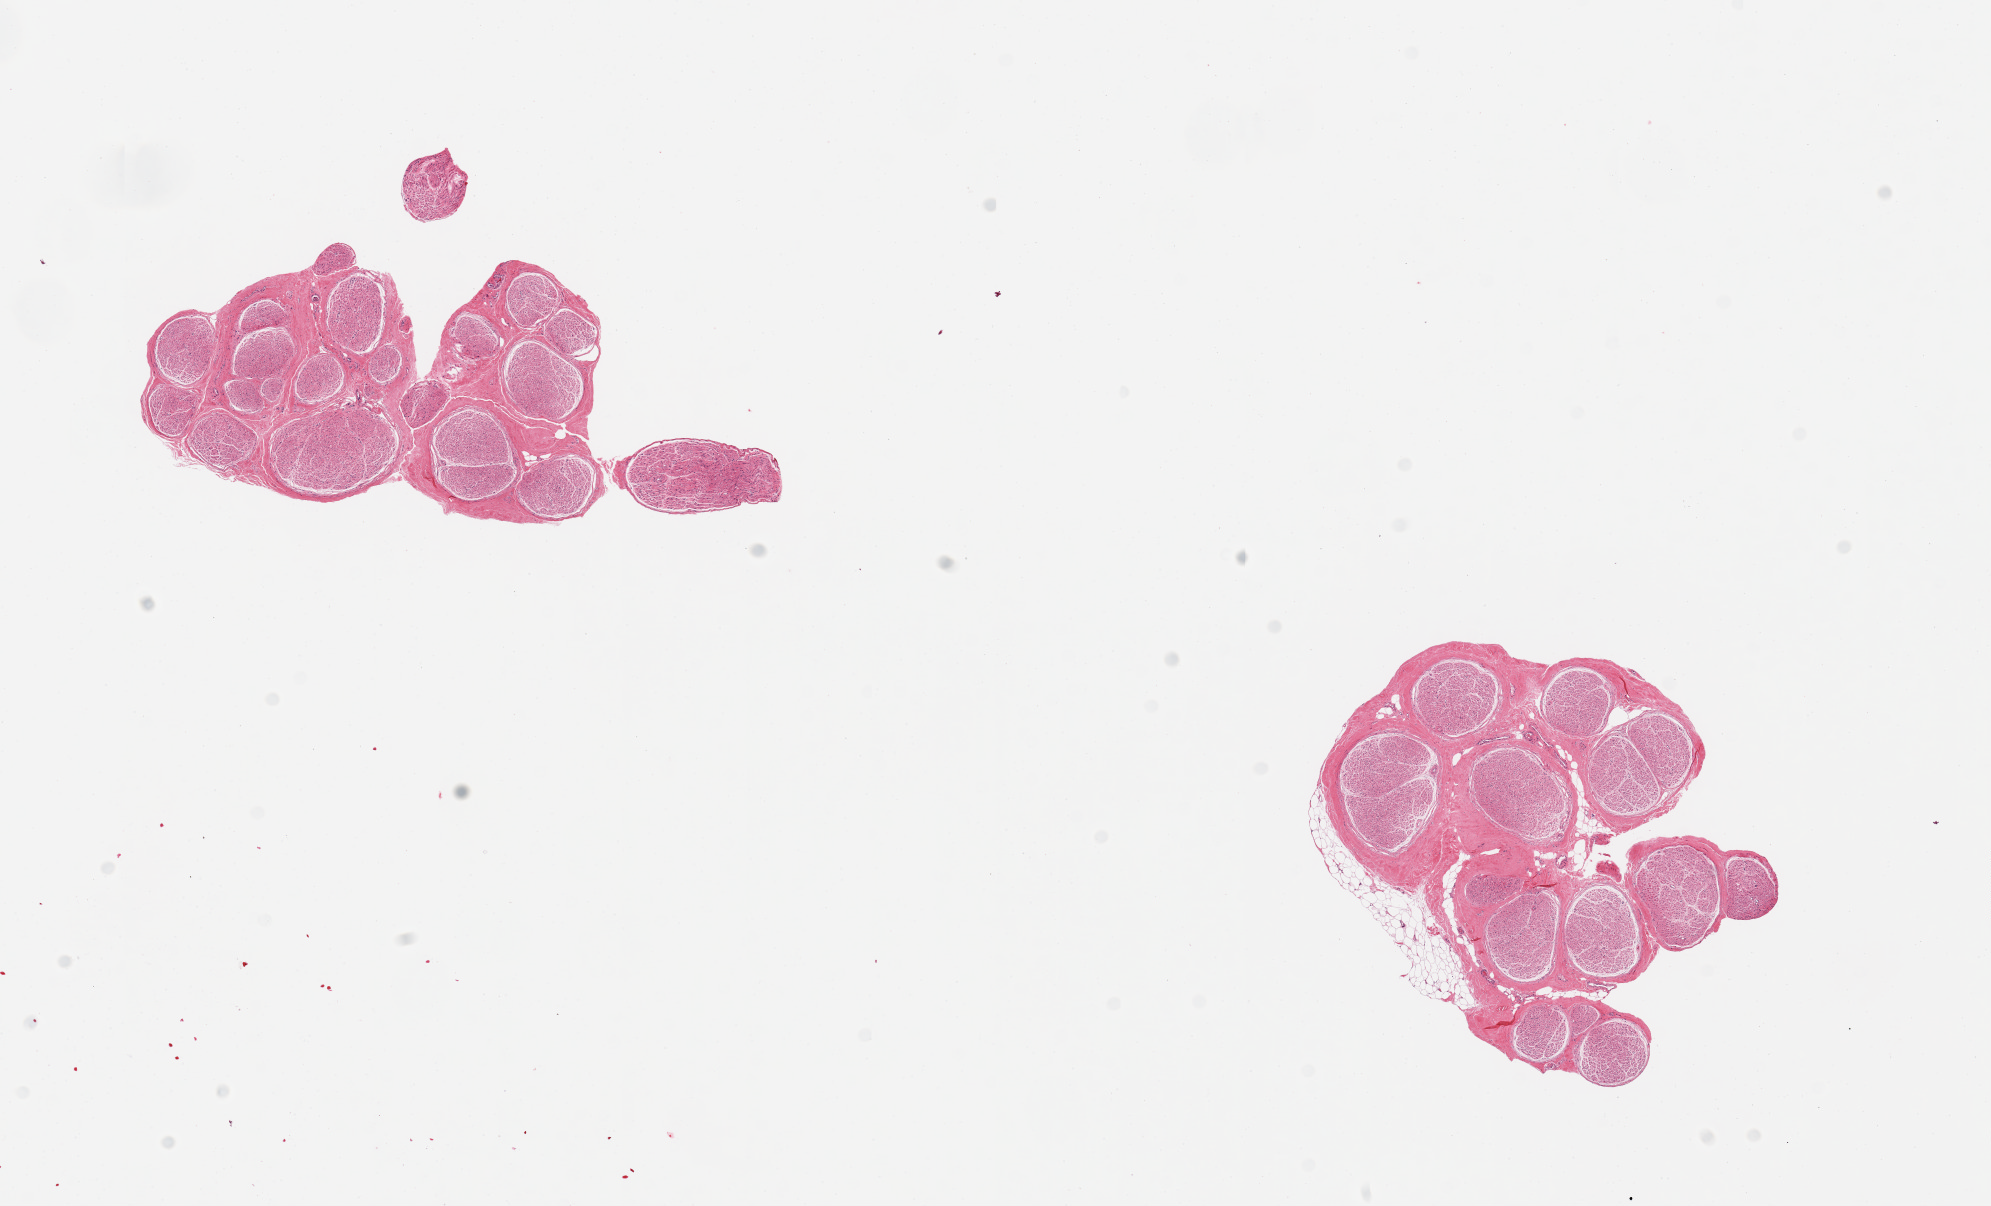
H&E whole-slide image, a low-resolution overview of the entire scanned area, about 15.8 x 9.5 mm; PAXgene-fixed, paraffin-embedded tissue; target tissue: tibial nerve; tissue donor sample. Male donor.
Review note (as recorded): 2 pieces; trivial attached fat on 1 piece.